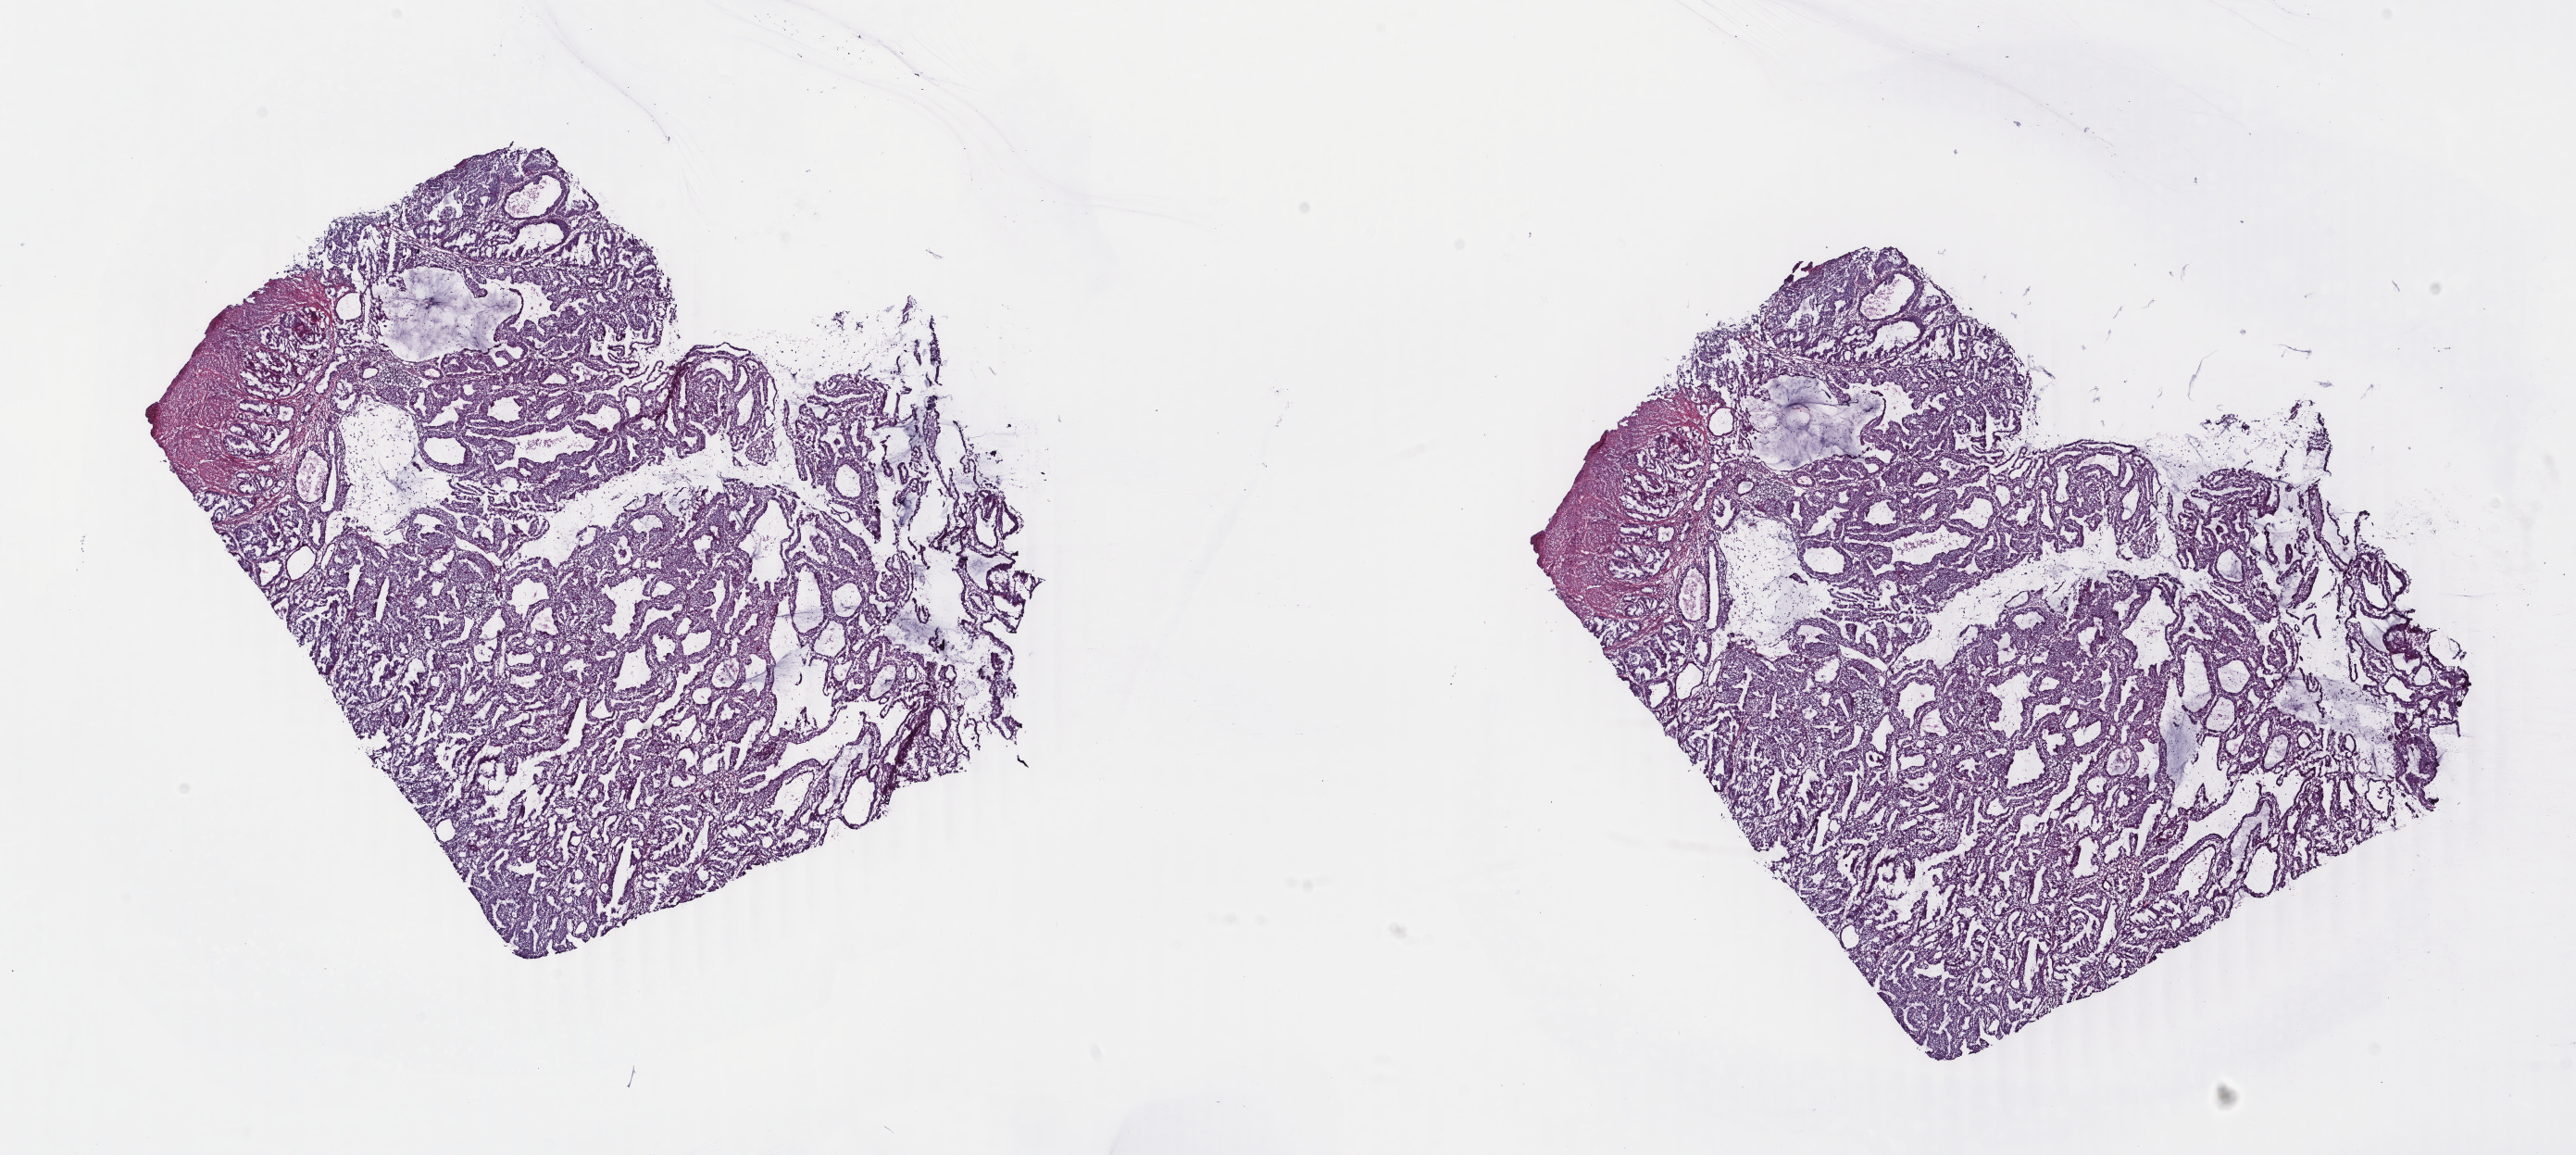
Digitized Hematoxylin and eosin (H&E) stained tissue section (whole slide) — low-resolution overview of the scanned area, about 22.1 x 9.9 mm; frozen section; uterus, primary tumour sample. Patient: female, age at initial diagnosis 81 years. Histologic grade: G1 (well differentiated). Slide review estimates, as recorded: tumour cells 83%, tumour nuclei 85%, normal cells 2%, stromal cells 15%, necrosis 0%. Inflammatory infiltration, as recorded: lymphocyte infiltration 12%, monocyte infiltration 0%, neutrophil infiltration 2%.
- diagnosis: Endometrioid adenocarcinoma, NOS
- FIGO stage: IA